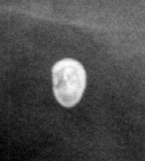
Crop from a digitized film mammogram around one marked abnormality, left breast, CC view.
- Finding: calcifications, morphology round and regular / lucent center / punctate, distribution diffusely scattered; BI-RADS assessment category 2; benign without callback (not worked up further).